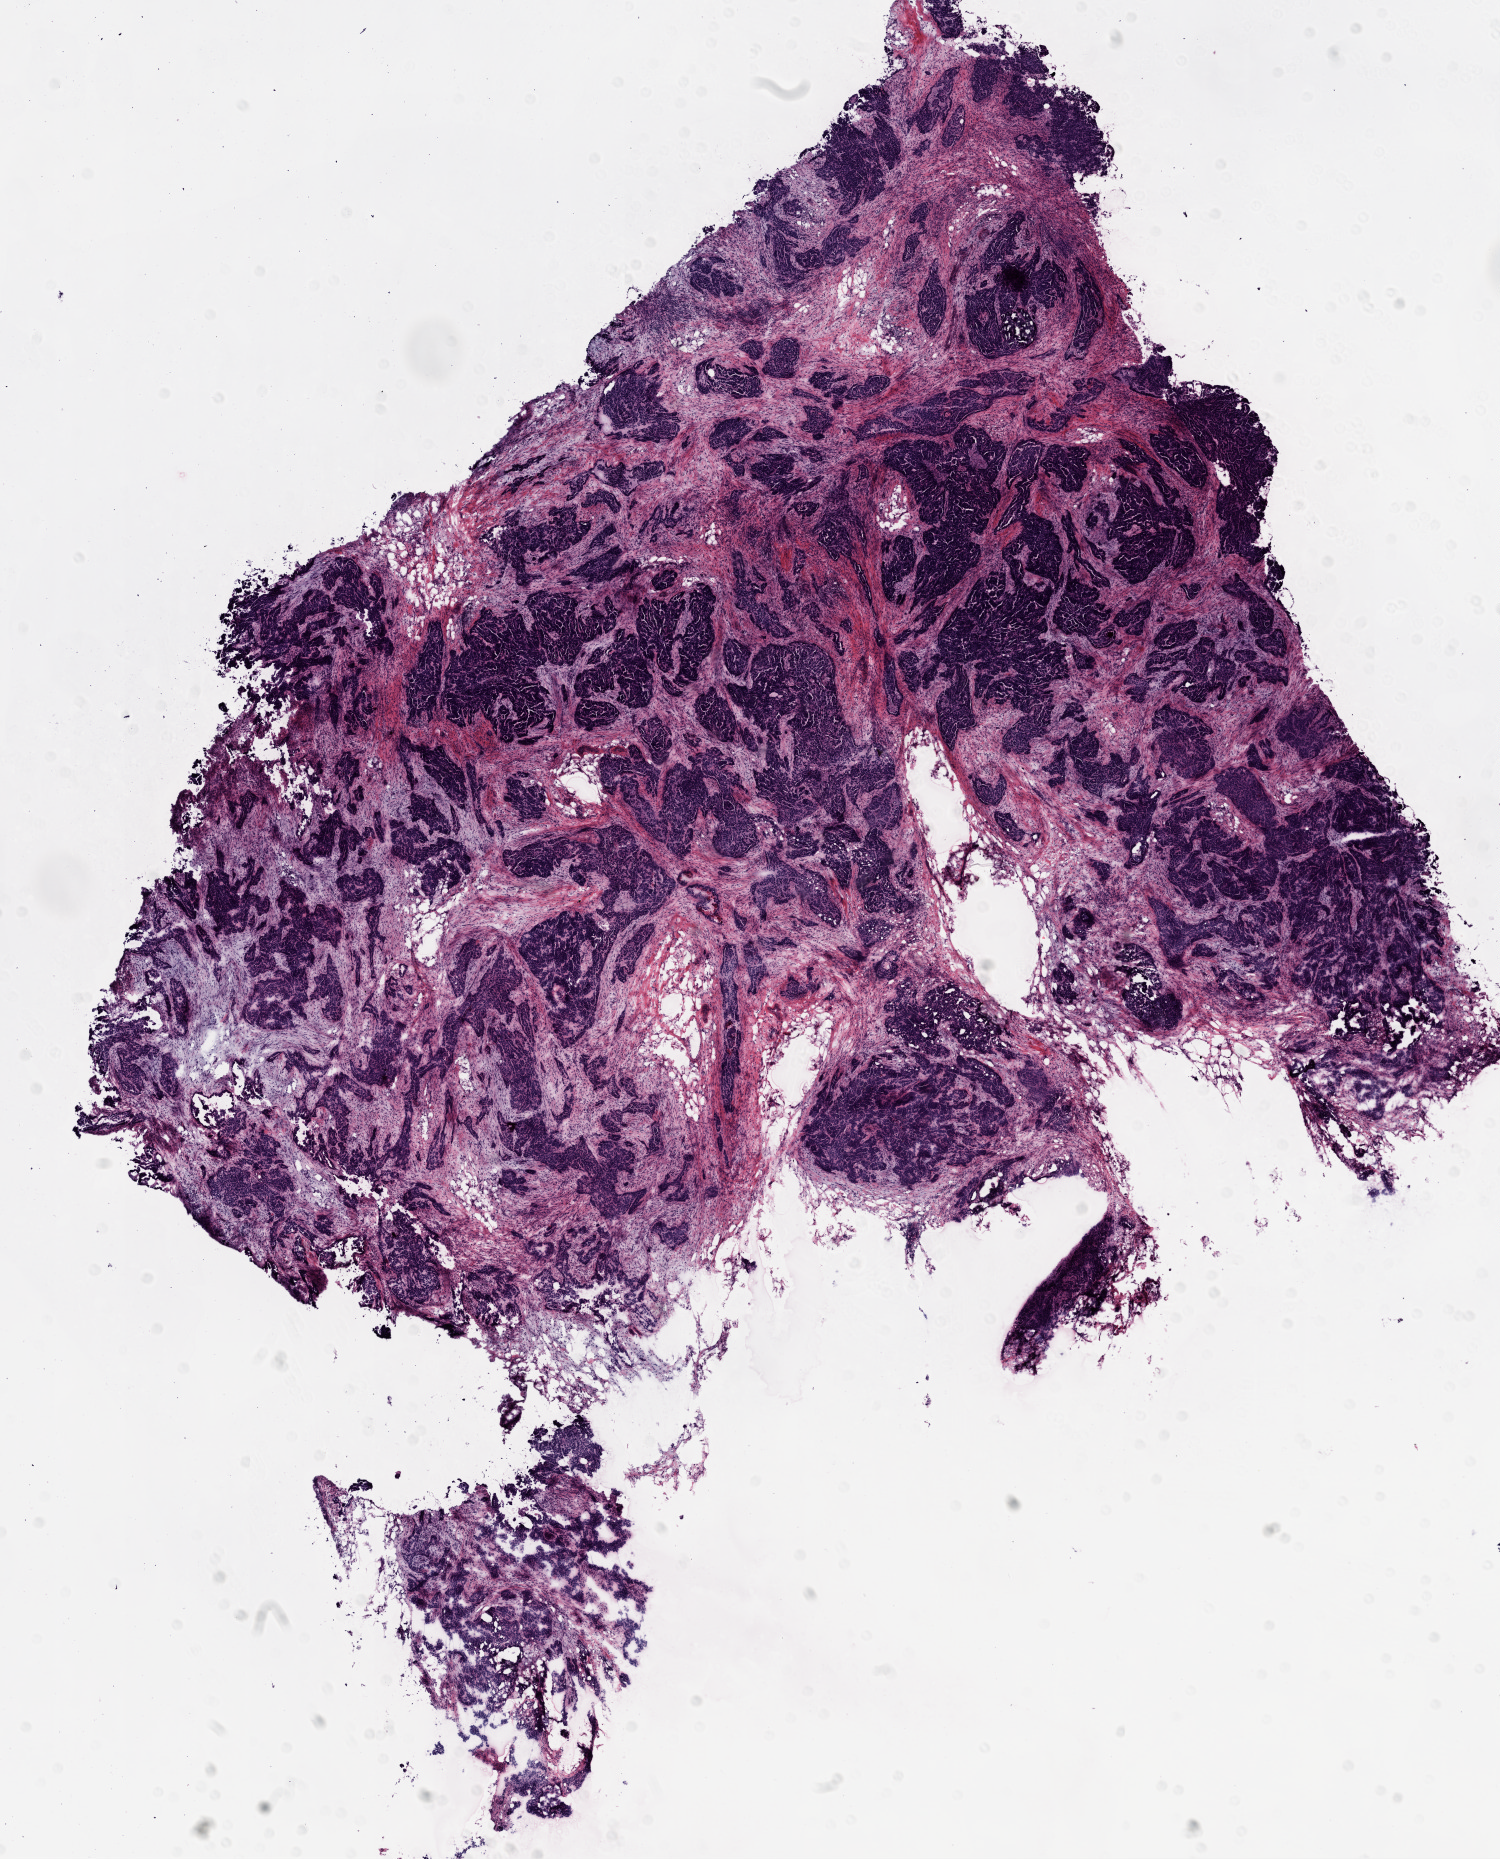
Digitized H&E tissue section (whole slide) — shown as a low-resolution overview of the whole scanned area (about 12.0 x 14.9 mm, from a 20x scan). Frozen section. Primary tumour sample from the ovary. Patient: female, age at initial diagnosis 63 years. Histologic grade: G3 (poorly differentiated). Pathologist review of this section (percent, as recorded): tumour cells 90%, tumour nuclei 90%, normal cells 0%, stromal cells 10%, necrosis 0%.
* FIGO stage: IIIC
* laterality: bilateral
* diagnosis: Serous cystadenocarcinoma, NOS